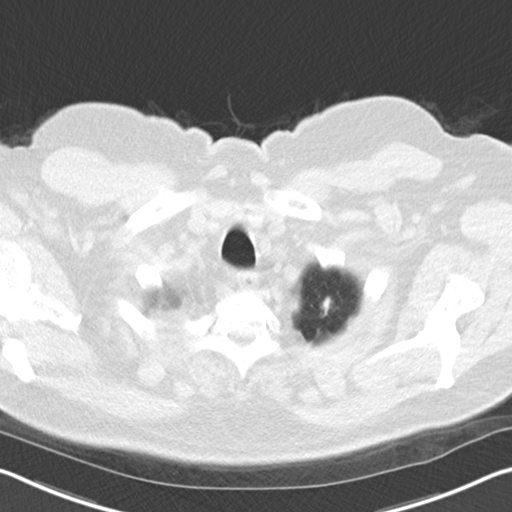
Low-dose screening chest CT, axial slice. Second annual screen. Lung window (W 1500 / L -600 HU). 5 mm slice thickness. 120 kVp. 512 × 512 image matrix, field of view 340 × 340 mm. Male, age 67 years at enrolment. Former smoker at enrolment.
Lesion marked by an expert reader, bounding box <307,293,344,327> (left, top, right, bottom; pixels). No non-calcified nodule or mass ≥4 mm was recorded by the screening reader at this exam. Participant outcome: lung cancer diagnosed 507 days after this screen — adenocarcinoma, NOS, left upper lobe, moderately differentiated (G2), stage IIA (AJCC 6th edition), 18 mm at pathology.